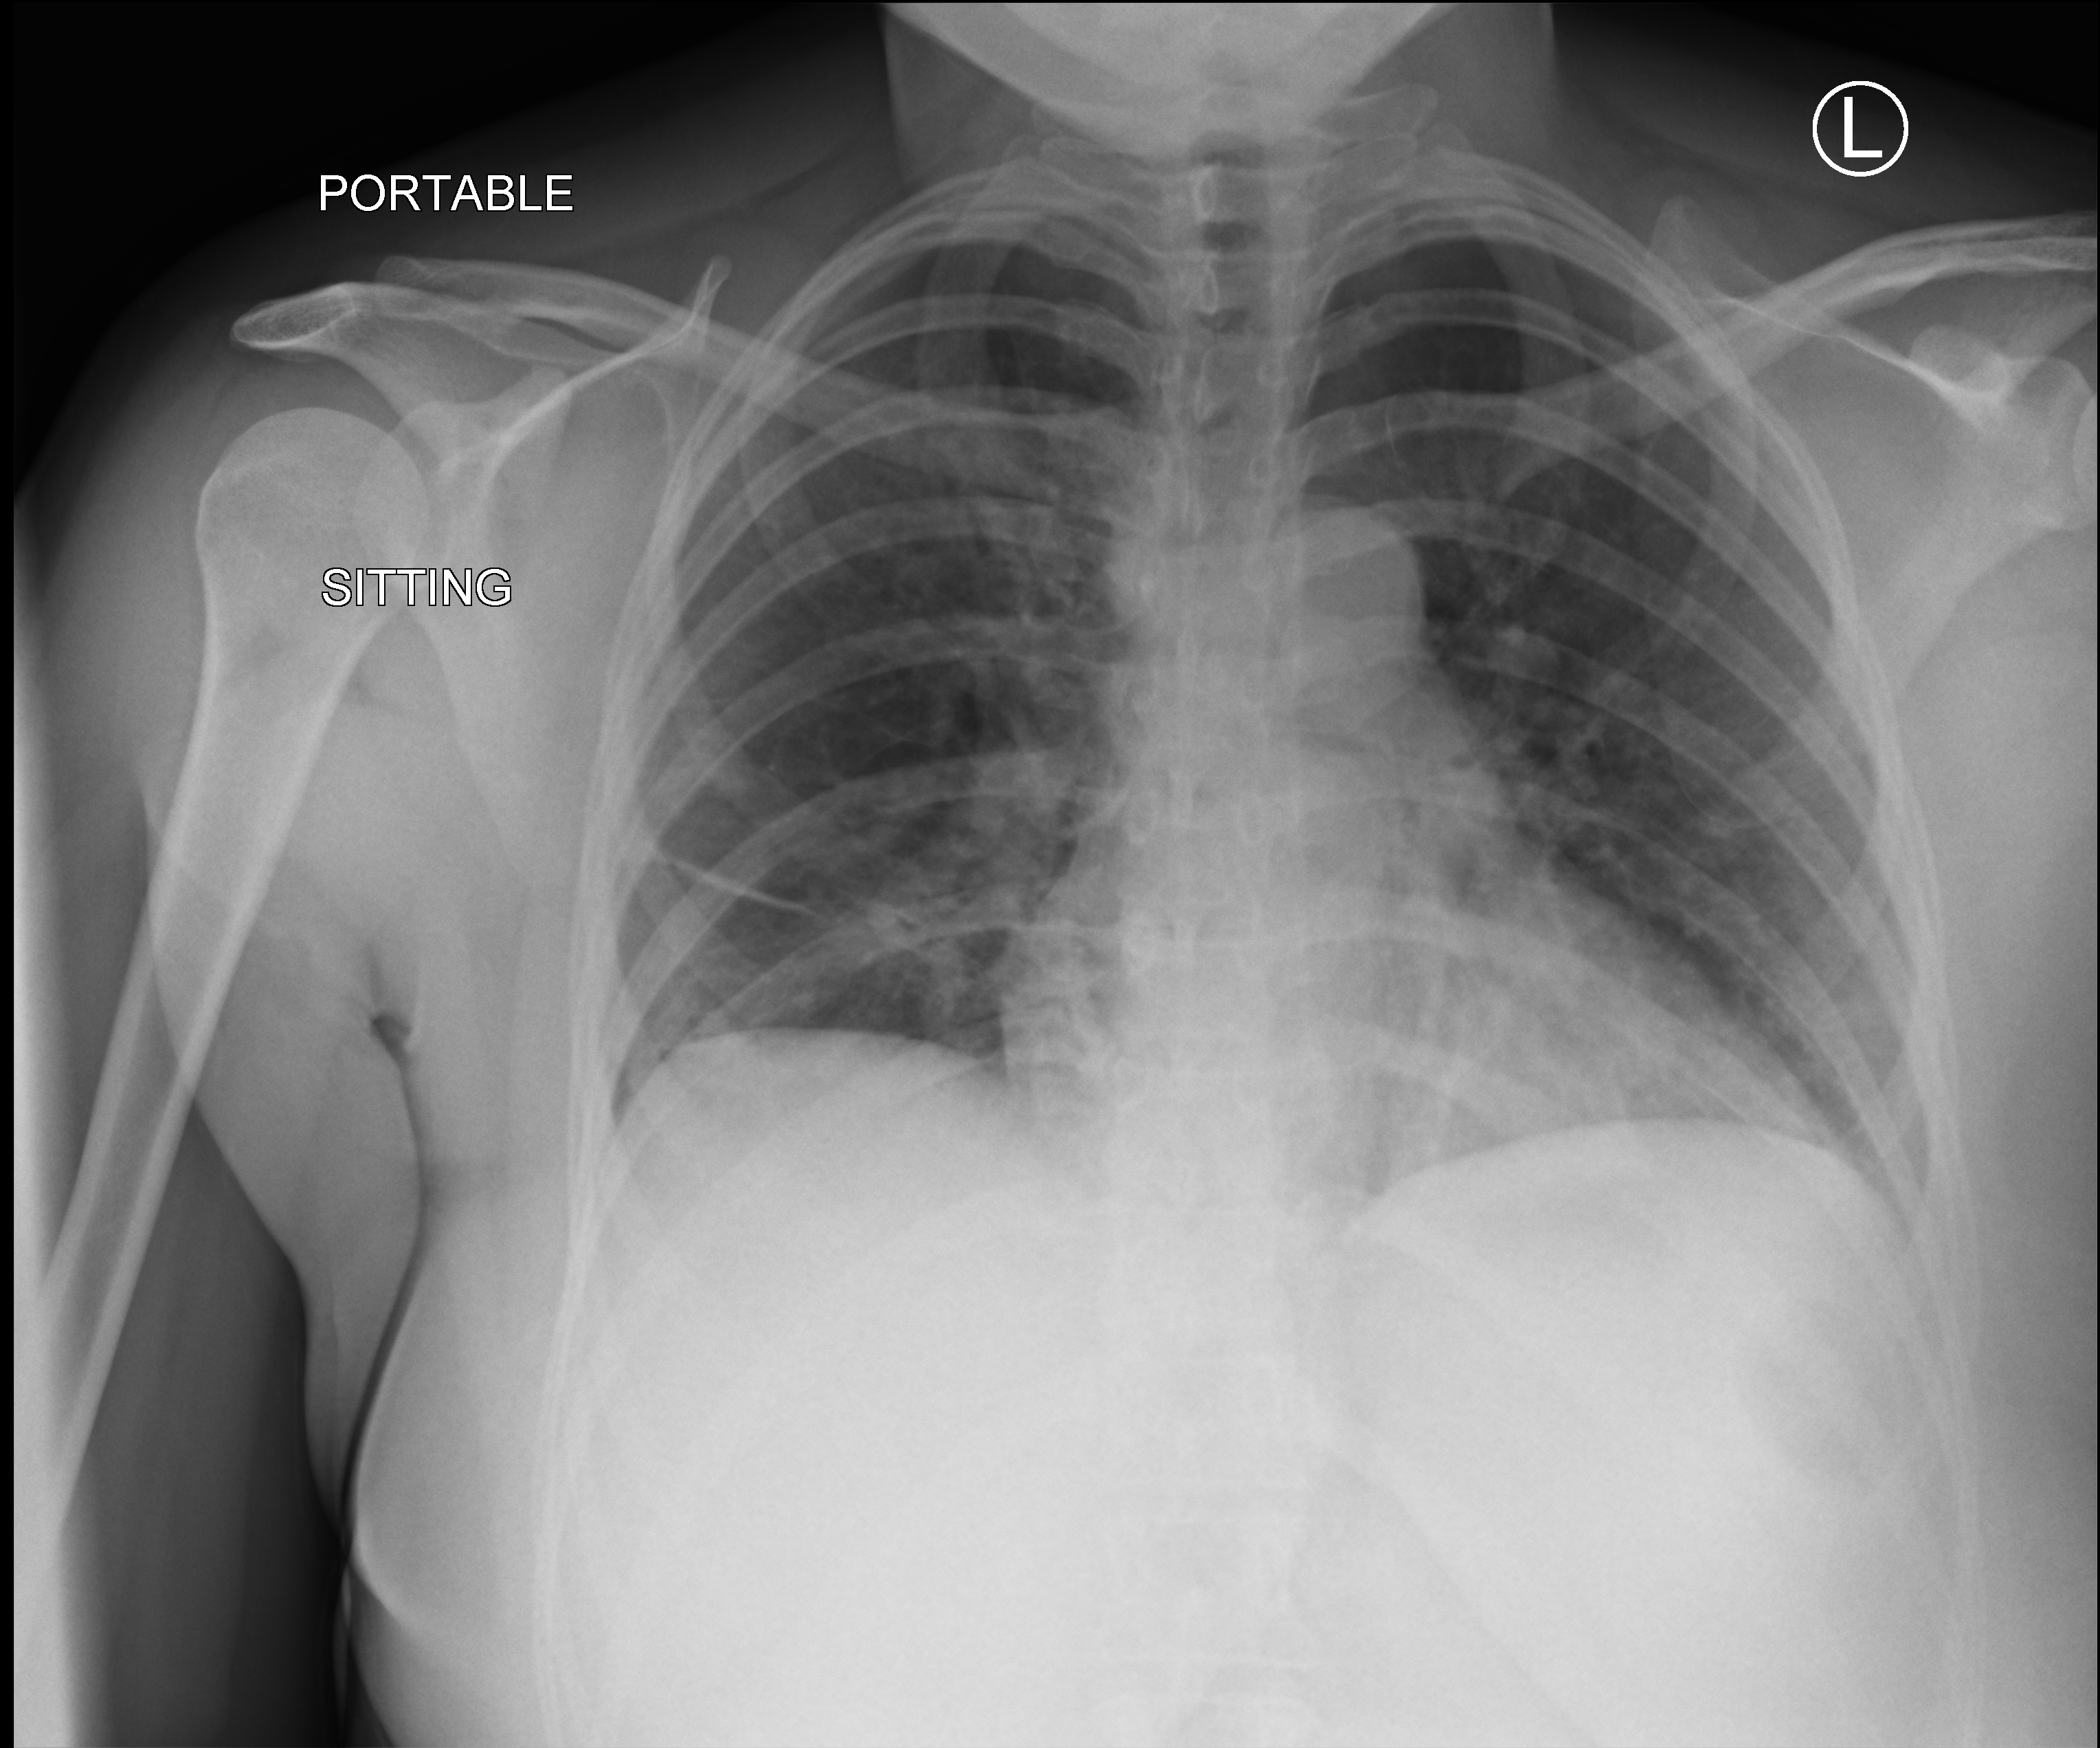
Portable chest radiograph; anteroposterior (AP) projection. Female patient hospitalised with COVID-19, age 18–59 years.
From the hospital-stay record, not from the radiograph (when in the stay this image was taken is not recorded): other chronic lung disease (admission record): no; length of hospital stay: 5 days.